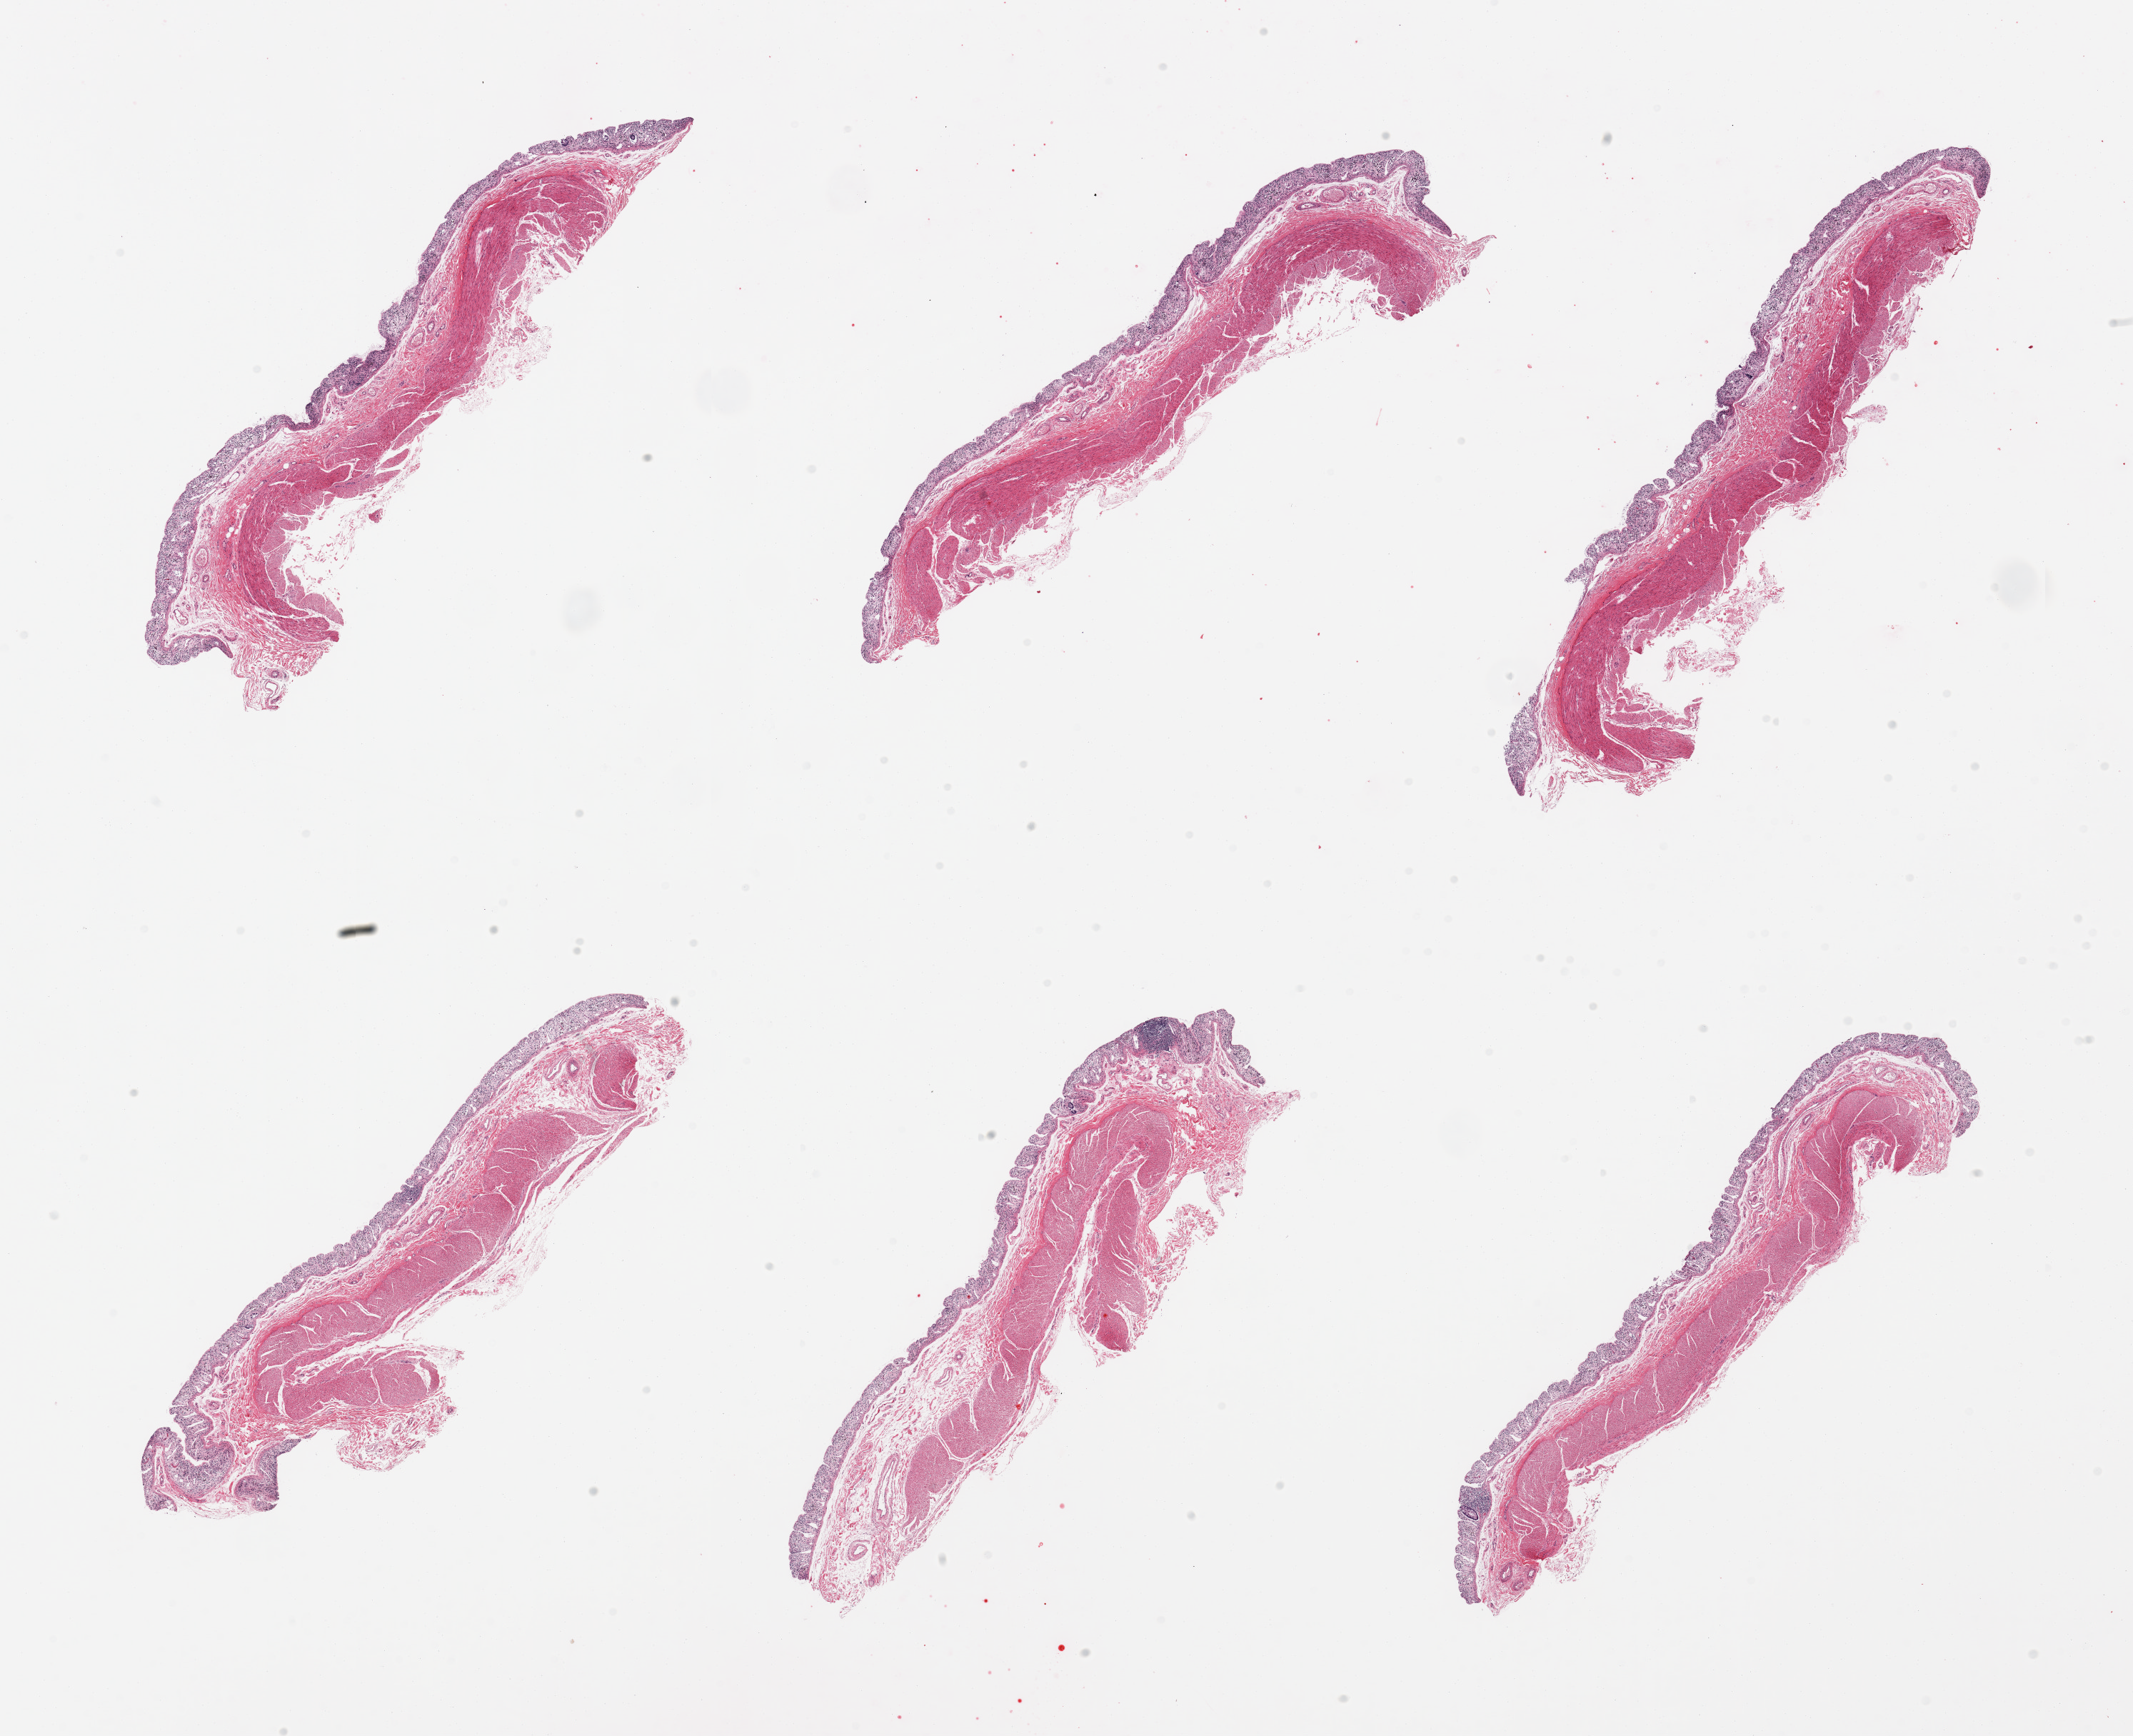
Digitized haematoxylin and eosin-stained section — a low-resolution overview of the entire scanned area, about 23.6 x 19.2 mm (acquisition: 20x scan), PAXgene-fixed, paraffin-embedded tissue, target tissue: transverse colon, donor tissue sample. Male donor.
Reviewer comment on this tissue sample: 6 pieces, mucosa is ~250microns; glandular elements totally autolyze/sloughed.